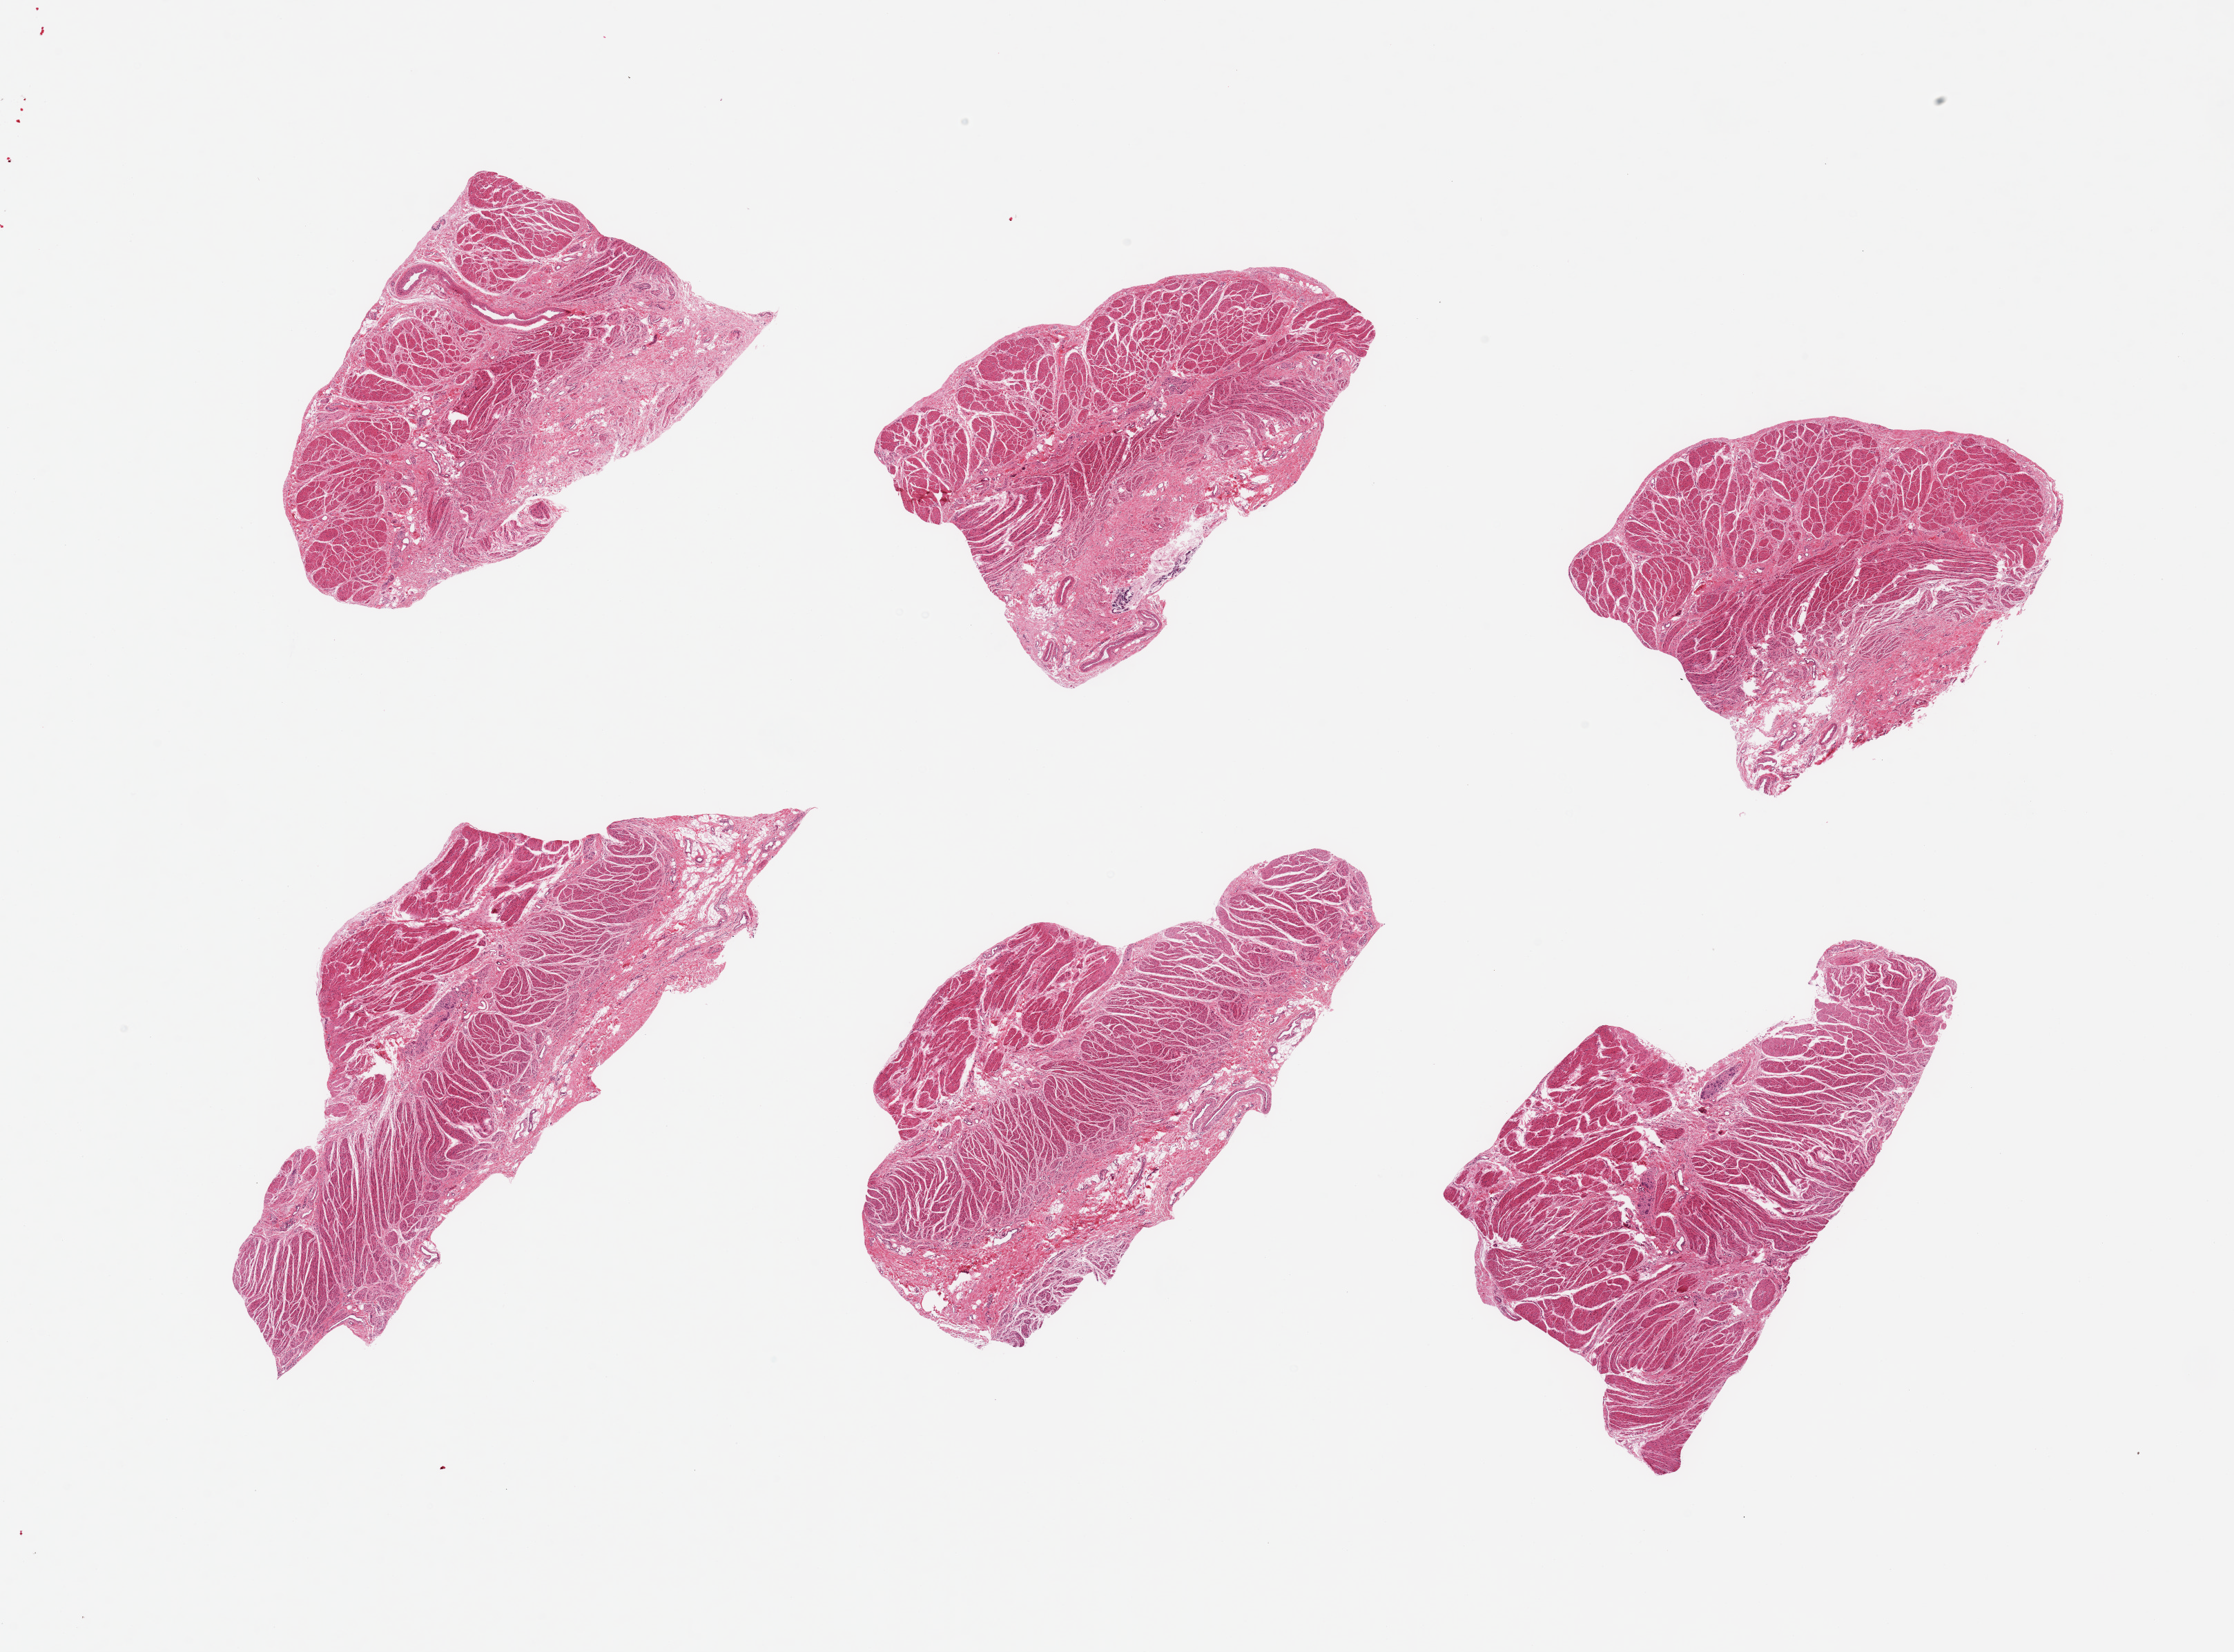
Whole-slide image, H&E stain, whole scanned area (about 25.6 x 18.9 mm) shown as a low-resolution overview. PAXgene-fixed paraffin-embedded (PFPE) section. Sampled site (target tissue): gastroesophageal junction. Tissue donor sample. Donor sex: male.
Review note (as recorded): 6 pieces, confirmed target muscularis.